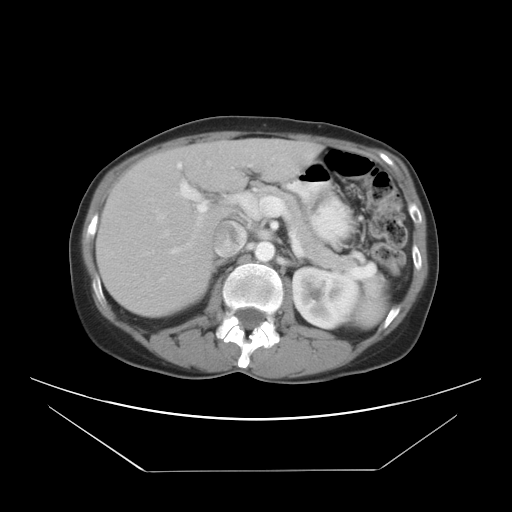
Contrast-enhanced abdominal CT, one axial slice; position 16 of 30 along the scan axis; intravenous contrast given; soft-tissue window (W 400 / L 40 HU); 512 × 512 image matrix, field of view 412 × 412 mm. Female patient, age 54 years. From the clinical record (not read from this slice): diagnosis: colorectal cancer liver metastases, imaged before liver resection; multiple liver metastases: yes; largest metastasis: 2.5 cm; disease in both lobes: yes.
Structures marked on this image (manually delineated by an expert):
- hepatic veins: bounding box (x1, y1, x2, y2) in pixels: (155, 210, 169, 300)
- liver: (99, 140, 318, 318)
- planned liver remnant (the part of the liver to remain after resection): (105, 142, 247, 318)
- portal vein (with intrahepatic branches): (168, 161, 207, 254)